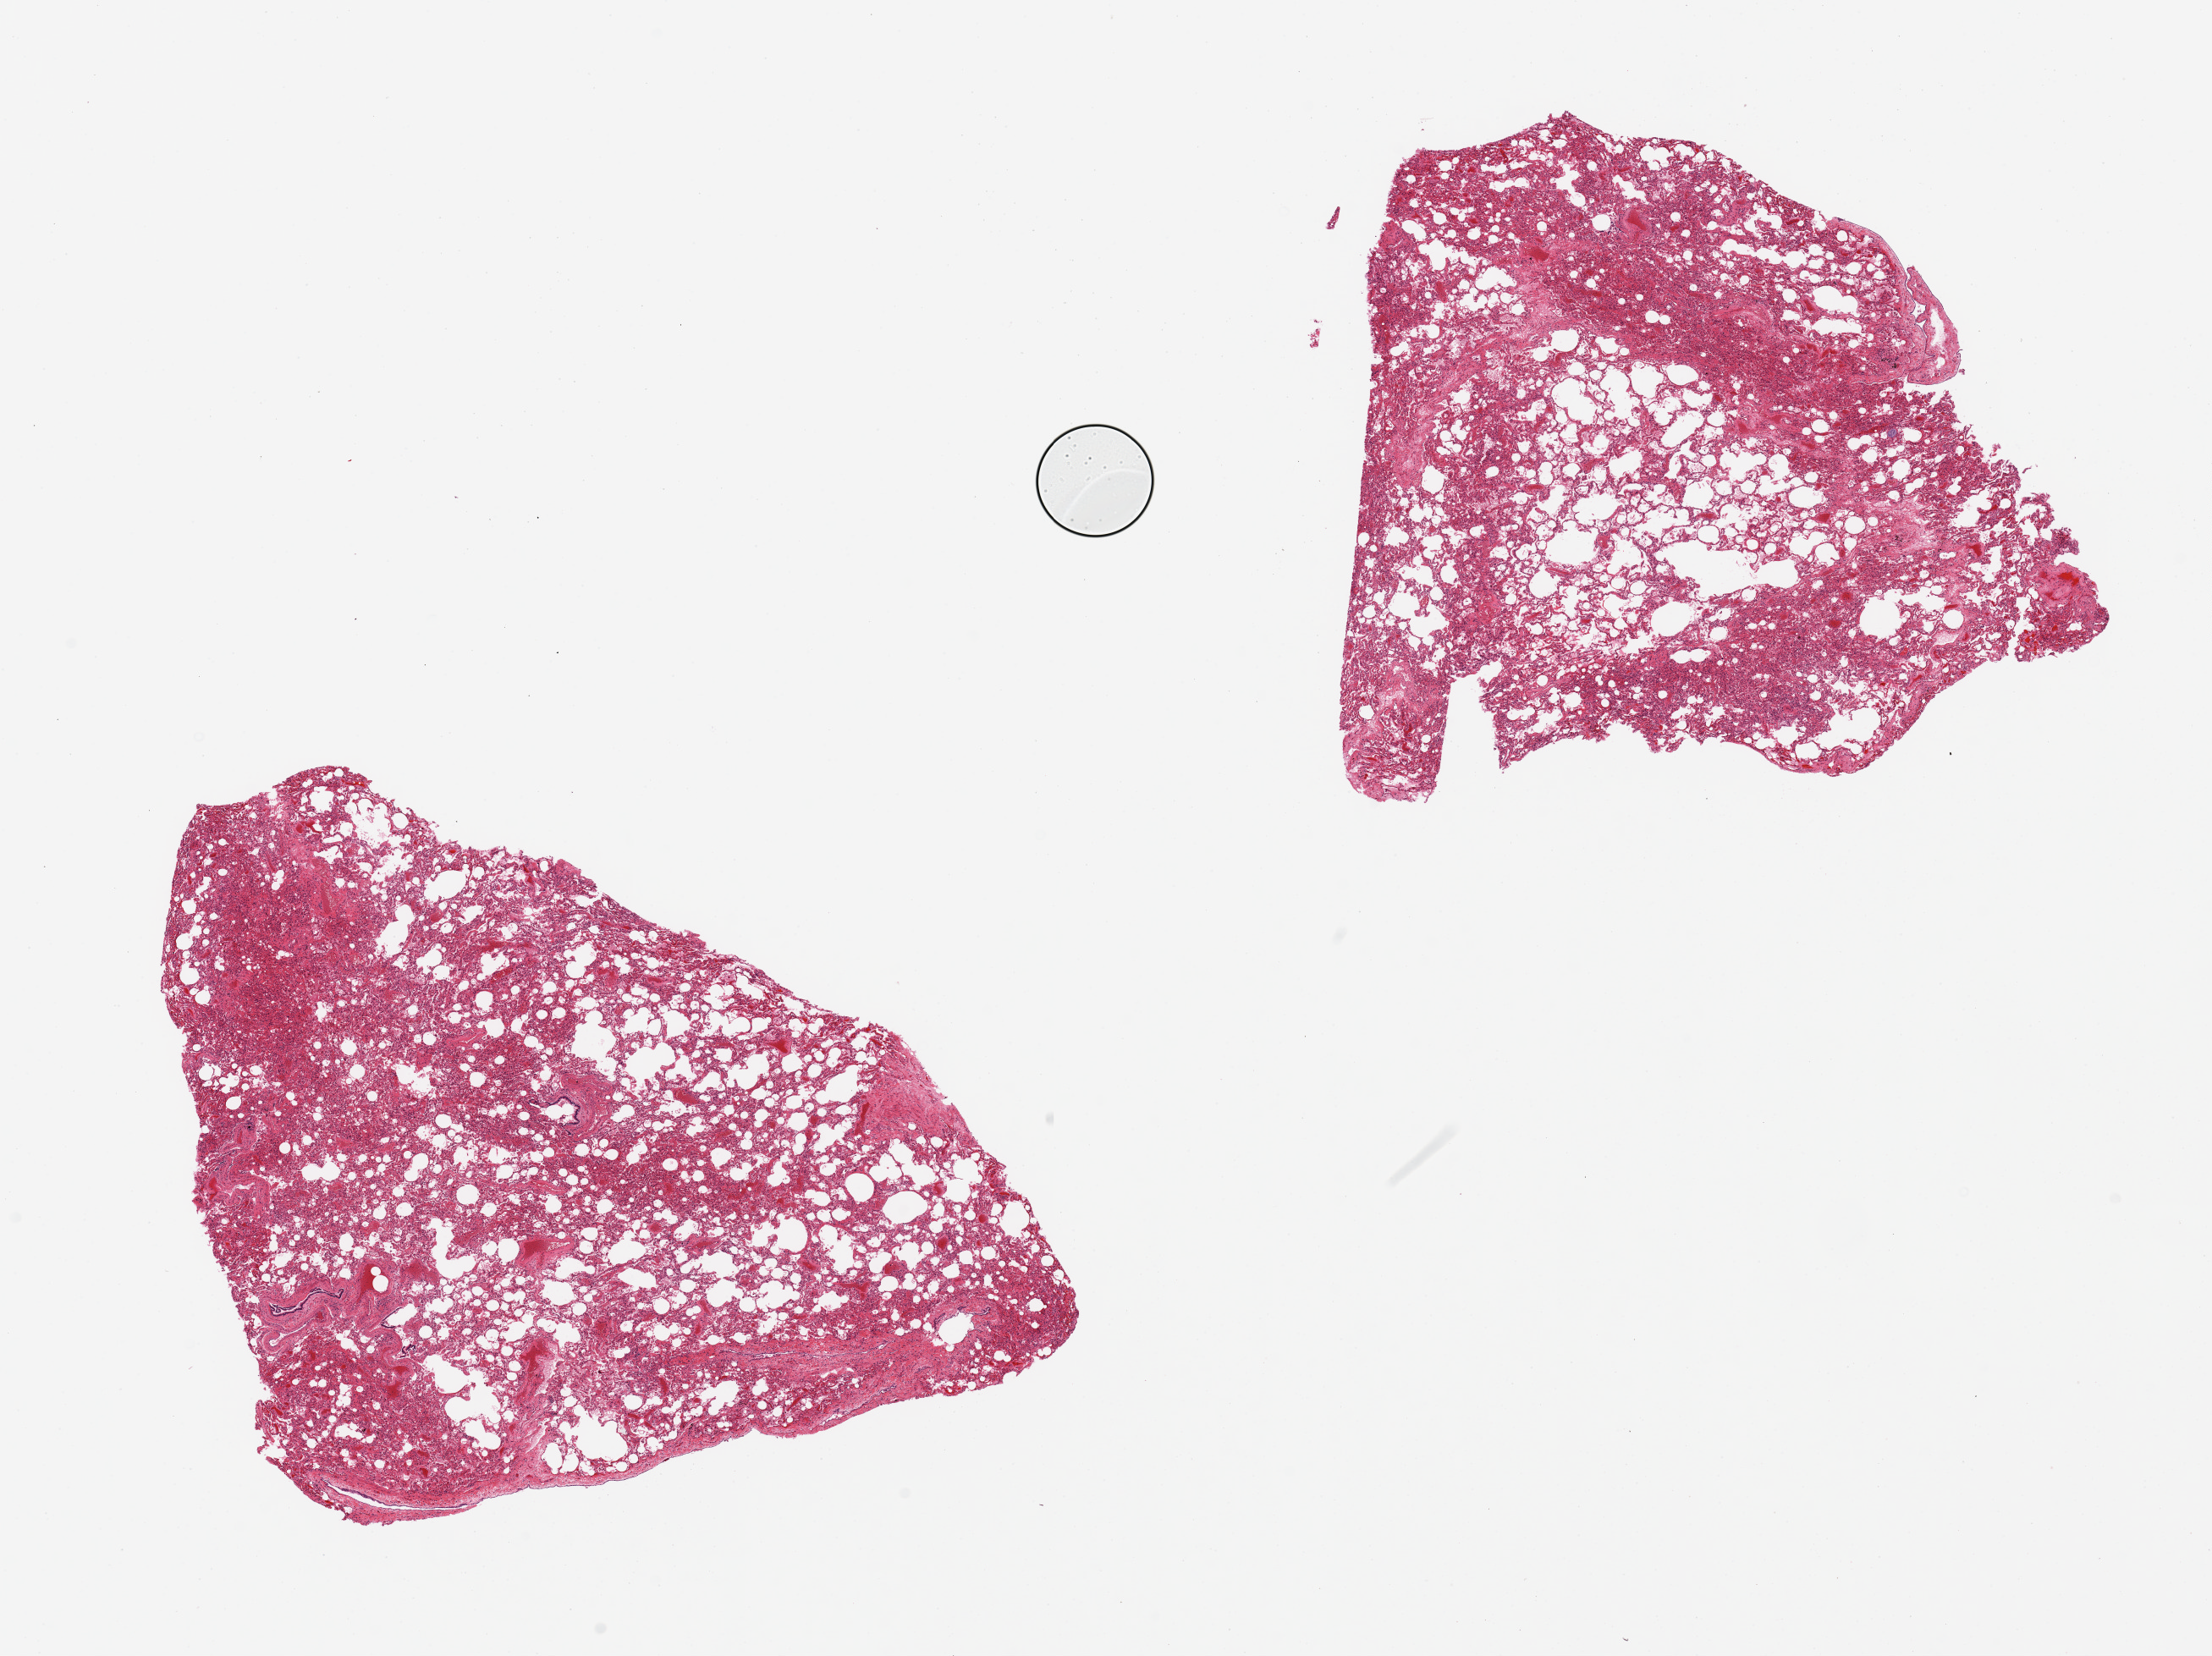
Digitized haematoxylin and eosin-stained section — low-resolution overview of the scanned area, about 20.7 x 15.5 mm; PAXgene-fixed paraffin-embedded (PFPE) section; section of lung (target tissue); tissue donor sample. Donor: female.
Review note (as recorded): 2 pieces, some congestion and emphysematous change and fibrosis.